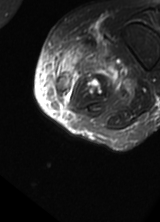
MRI of an extremity soft-tissue mass, one axial slice; slice 8 of 69 in the series (ordered by position); T2-weighted fat-saturated; MR volume resampled by the dataset authors to the PET/CT grid (not the native acquisition matrix); 160 × 222 image matrix, field of view 156 × 217 mm. Female patient. Case-level facts recorded for this patient, not image findings: histological type: pleomorphic leiomyosarcoma; grade: high; site of the primary tumour: left thigh.
Outlined on this slice (expert contour drawn on MRI and transferred to this co-registered scan by the dataset authors):
- gross tumour volume including surrounding oedema: bounding box [x1, y1, x2, y2] px = [55, 36, 135, 101]